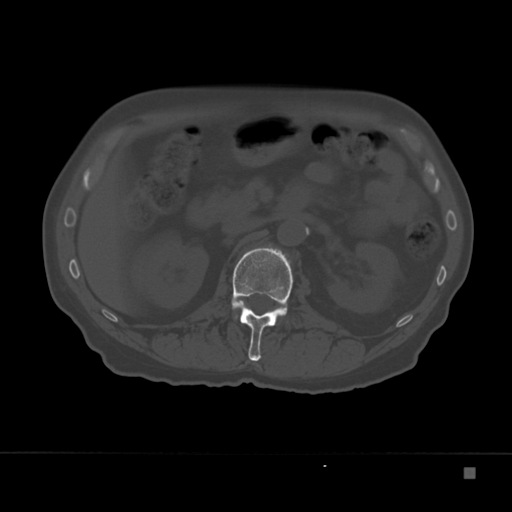
CT including the spine, one axial slice. Position 107 of 332 along the scan axis. Reconstruction kernel Br40s. Bone window (W 1800 / L 400 HU). 1.5 mm slice thickness. 512 × 512 image matrix, field of view 389 × 389 mm. Patient: male, 72 years. Case-level facts recorded for this patient, not image findings: primary cancer: skeletal.
Structures marked on this image (semi-automatically segmented with operator editing):
- L1 vertebra: bounding box [x1, y1, x2, y2] px = [232, 247, 293, 362]
- L2 vertebra: [235, 316, 237, 318]